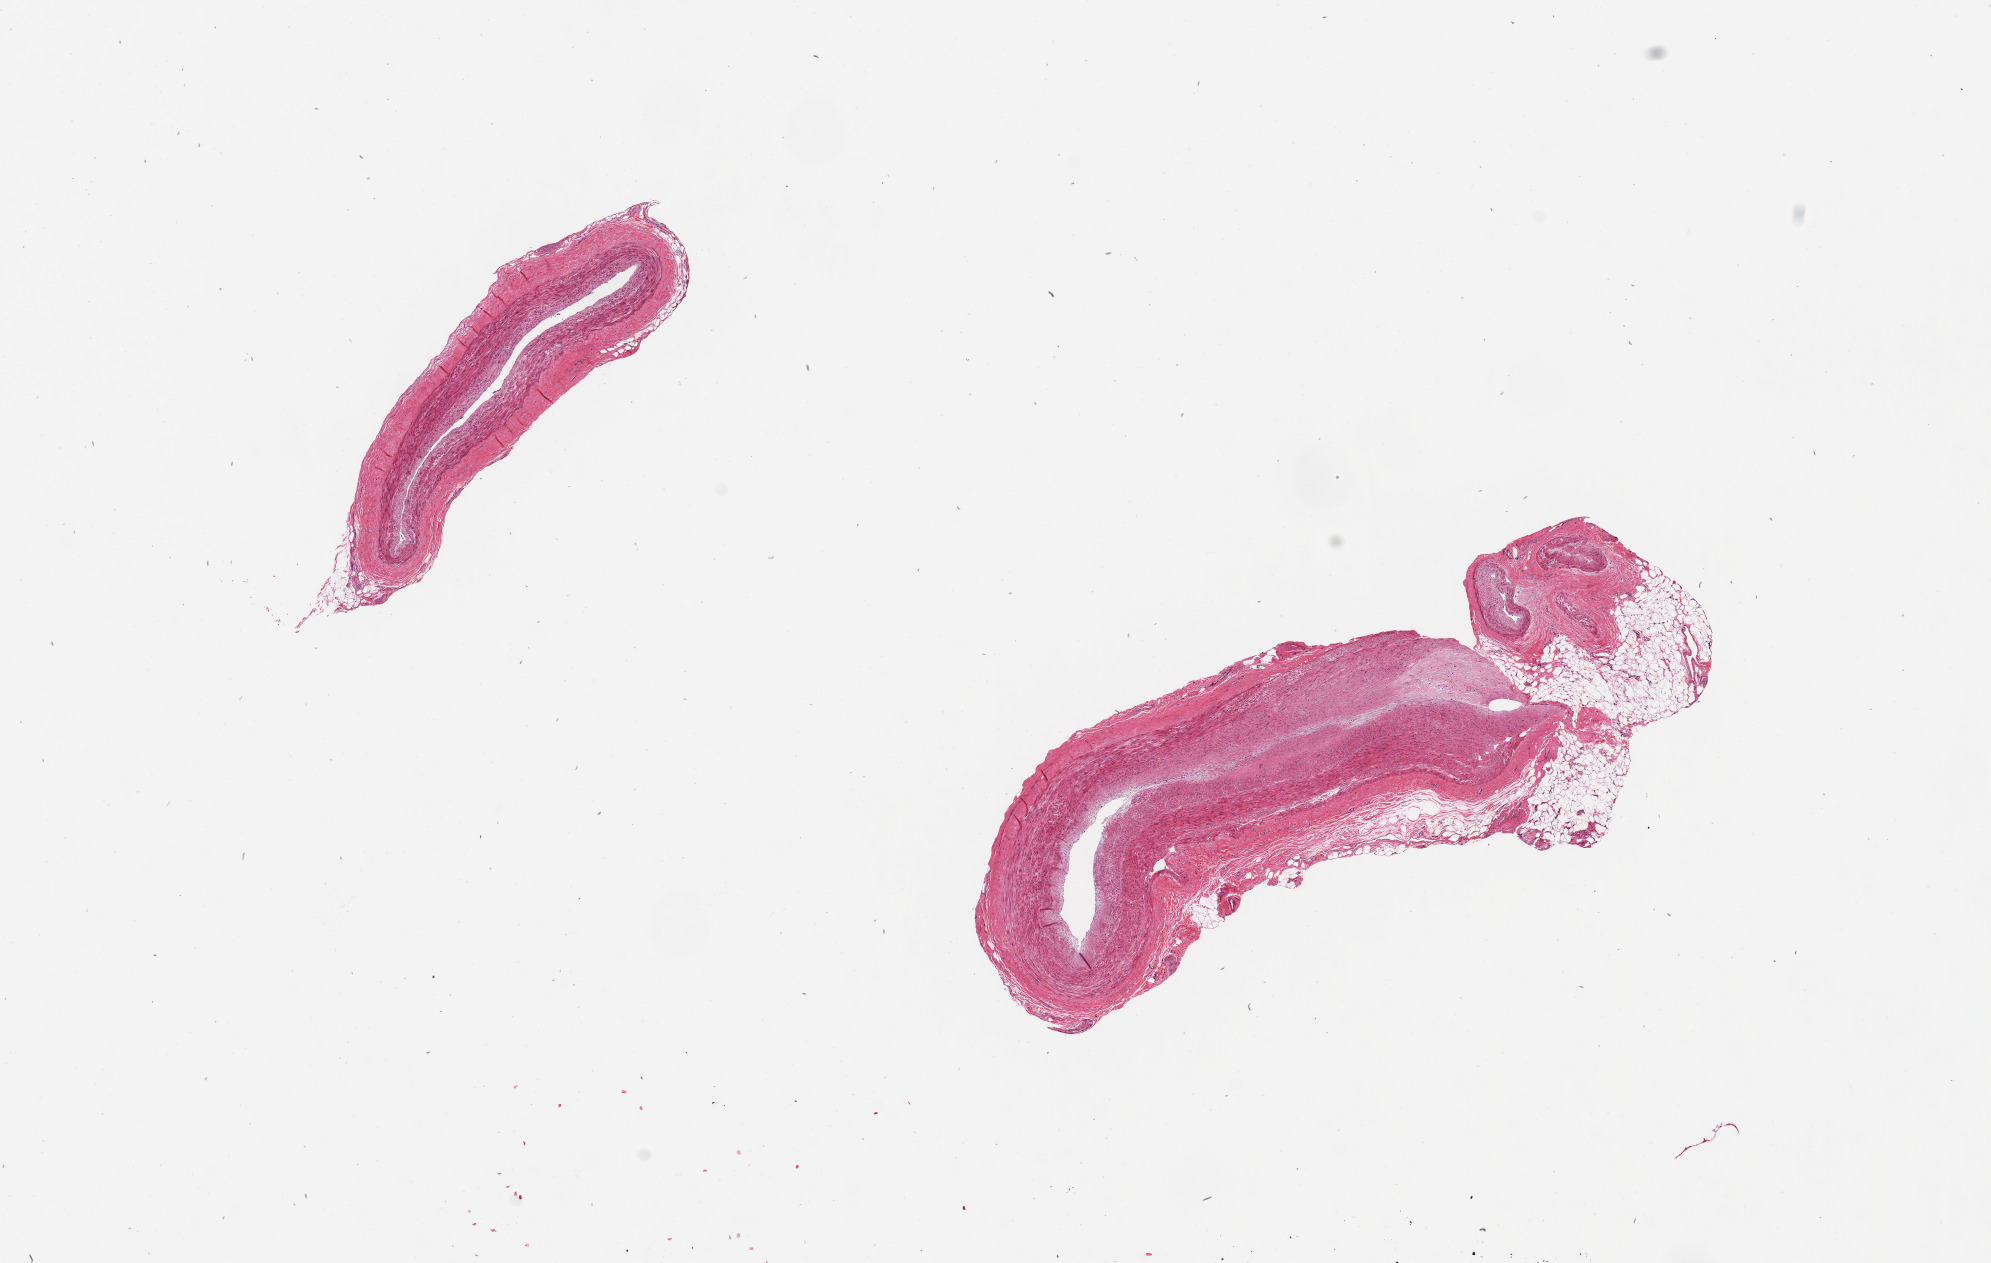
Whole-slide image, haematoxylin and eosin stain, brightfield — whole scanned area (about 15.8 x 10.0 mm, acquisition: 20x scan) shown as a low-resolution overview; PAXgene-fixed paraffin-embedded (PFPE) section; sampled site (target tissue): coronary artery; donor tissue sample. Female donor.
- reviewer comment on this tissue sample: 2 pieces, 4x1 & 6x2mm; fibrous plaques